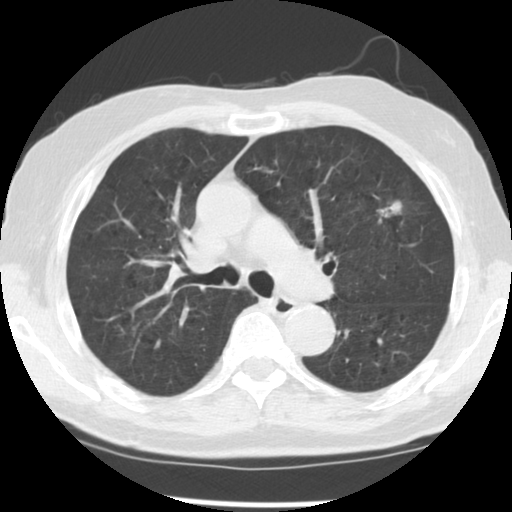
Low-dose screening chest CT, one axial slice; slice 82 of 131 in the series (ordered by position); 140 kVp; lung window (W 1500 / L -600 HU); 512 × 512 image matrix.
Structures marked on this image (outlined manually by an expert reader):
- lesion 1 (tumor, upper lobe of left lung): box from (x=379, y=201) to (x=402, y=217) px